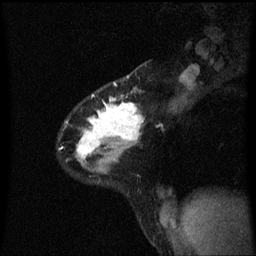
Breast MRI (dynamic contrast-enhanced), one sagittal slice; slice 43 of 60 in the series (ordered by position); dynamic contrast-enhanced series, image 2 of 3 at this slice position (ordered by acquisition); 1.5 T; TE 4.2 ms, TR 8.4 ms; 2 mm slice thickness; 256 × 256 image matrix. Female patient, age 32 years.
Annotated regions visible in this slice (semi-automatic segmentation, software-assisted and operator-edited):
- analysis volume of interest (the breast-tissue region the enhancement analysis was run in; not a lesion): bounding box [x1, y1, x2, y2] px = [60, 76, 144, 169]
- tumour enhancement mask (voxels above the 70 % enhancement threshold inside the analysis volume of interest): [77, 94, 144, 159]